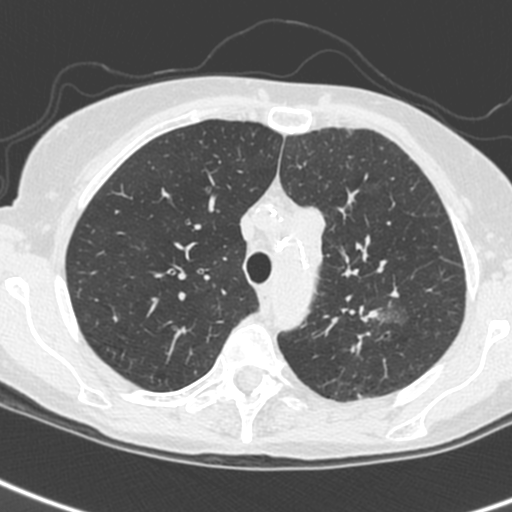
Low-dose screening chest CT, one axial slice. Slice 189 of 242 in the series (ordered by position). Lung window (W 1500 / L -600 HU). 512 × 512 image matrix.
Outlined on this slice (expert manual segmentation):
- lesion 3 (tumor, upper lobe of left lung): bounding box [x1, y1, x2, y2] px = [297, 207, 325, 274]